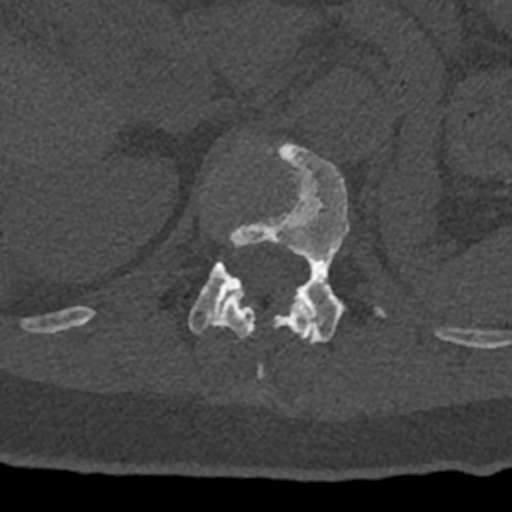
CT including the spine, one axial slice. Position 459 of 797 along the scan axis. Reconstruction kernel Br40s/3. 120 kVp. Bone window (W 1800 / L 400 HU). 512 × 512 image matrix. Male patient, age 74 years. From the clinical record (not read from this slice): primary cancer: renal; vertebrae with lytic lesions (as recorded): T10, L1, L2, L3, L4, L5.
Annotated regions visible in this slice (semi-automatic segmentation, software-assisted and operator-edited):
- L1 vertebra: bounding box <188,142,385,344> (left, top, right, bottom; pixels)
- T12 vertebra: <70,295,312,379>